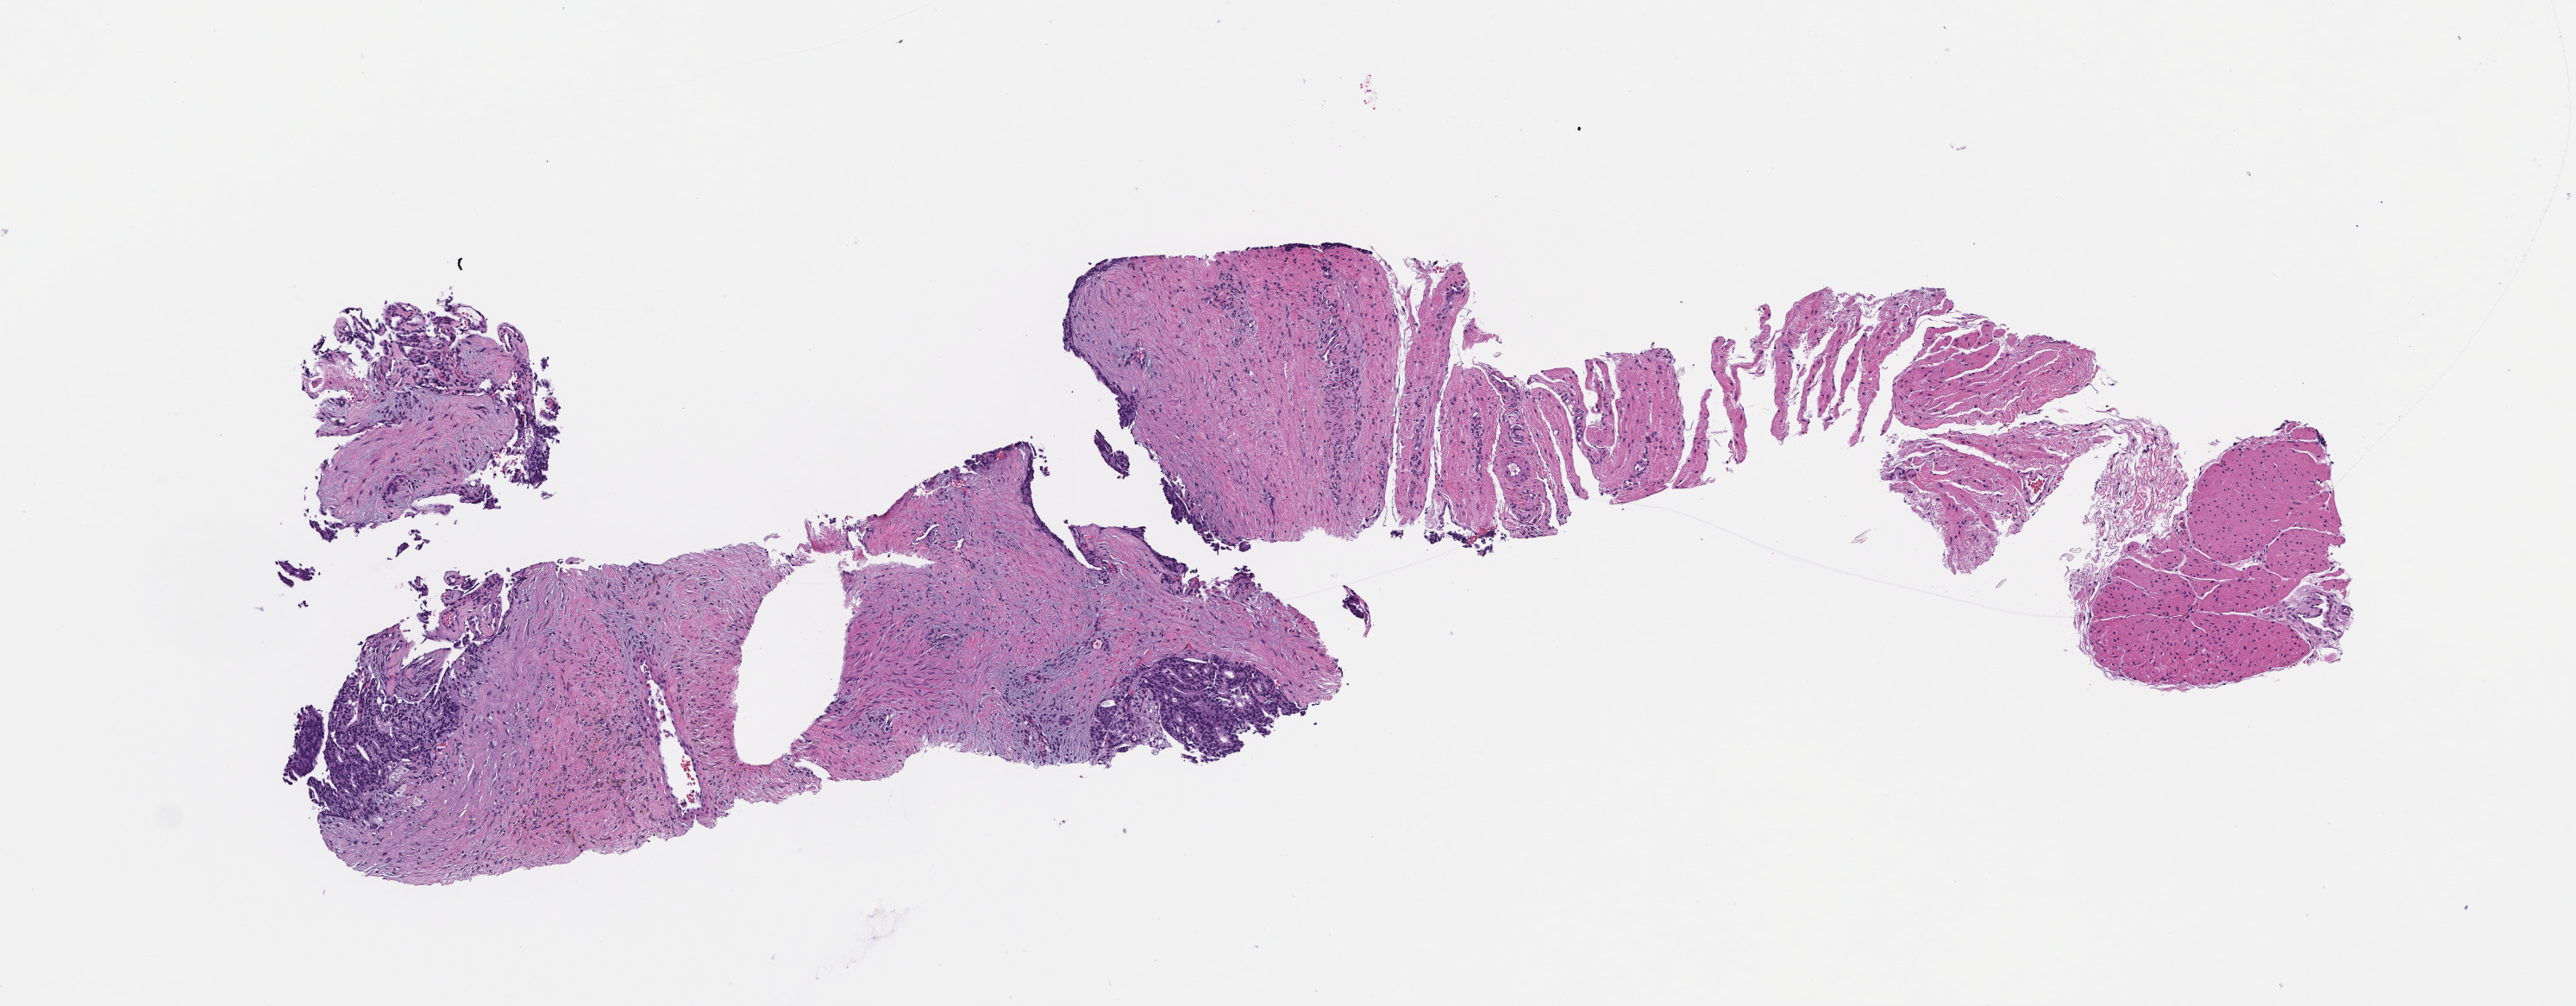
Whole-slide image, haematoxylin and eosin stain — whole scanned area (about 6.0 x 2.4 mm) shown as a low-resolution overview; FFPE section; tissue site: prostate; specimen time point: archival tissue. Male patient.
This section: primary tumor. Diagnosis: Prostate Carcinoma.